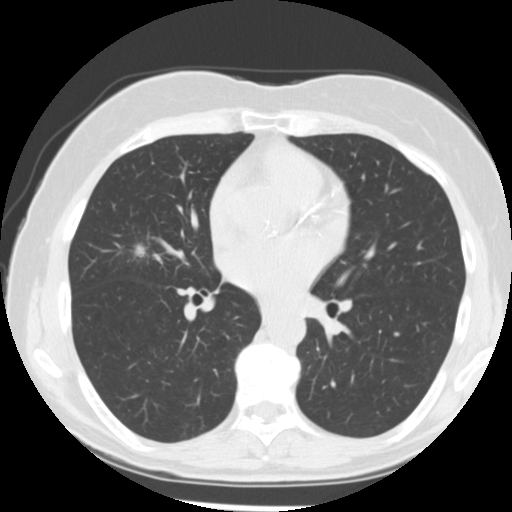
Low-dose screening chest CT, one axial slice; position 139 of 255 along the scan axis; 120 kVp; lung window (W 1500 / L -600 HU); 2.5 mm slice thickness; 512 × 512 image matrix.
Structures marked on this image (outlined manually by an expert reader):
- lesion 1 (tumor, middle lobe of right lung): bounding box [x1, y1, x2, y2] px = [135, 245, 145, 257]